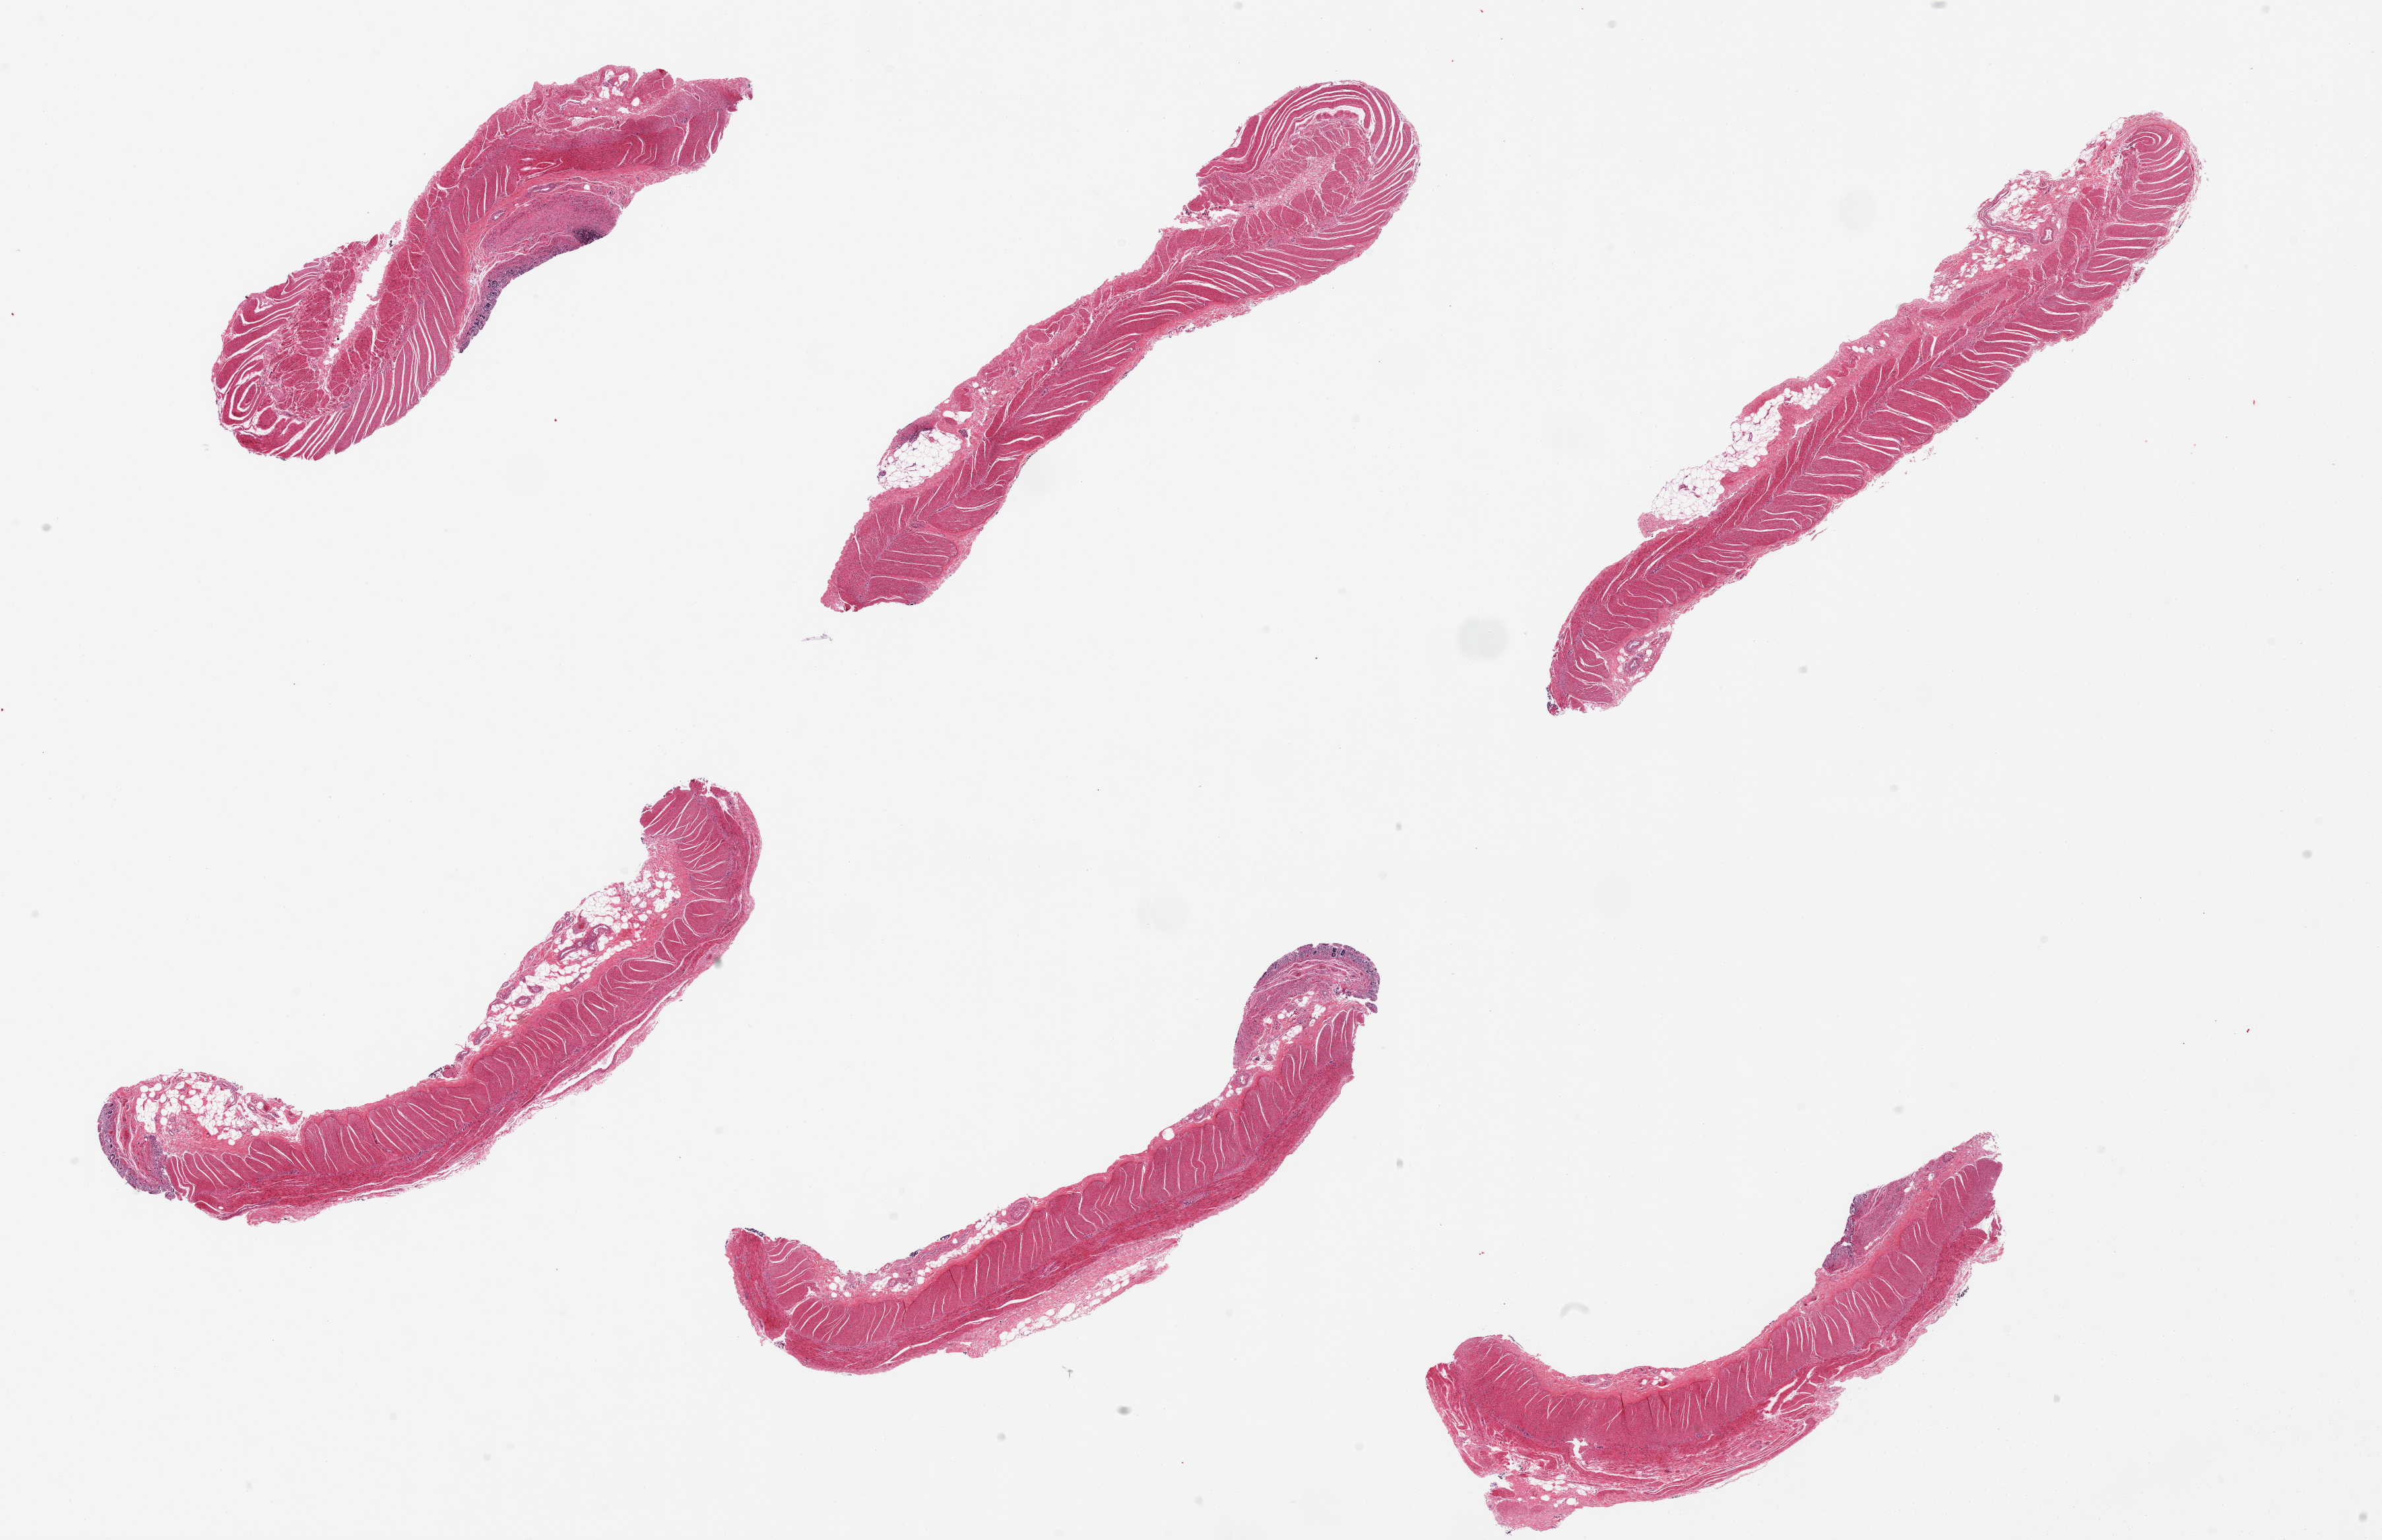
Digitized haematoxylin and eosin-stained section, a low-resolution overview of the entire scanned area, about 28.5 x 18.5 mm. PAXgene-fixed, paraffin-embedded tissue. Target tissue: ileum. Tissue donor sample. Male donor.
Reviewer comment on this tissue sample: 6 pieces; mostly muscularis (not target) minimal mucosa, virtually no lymphoid tissue.